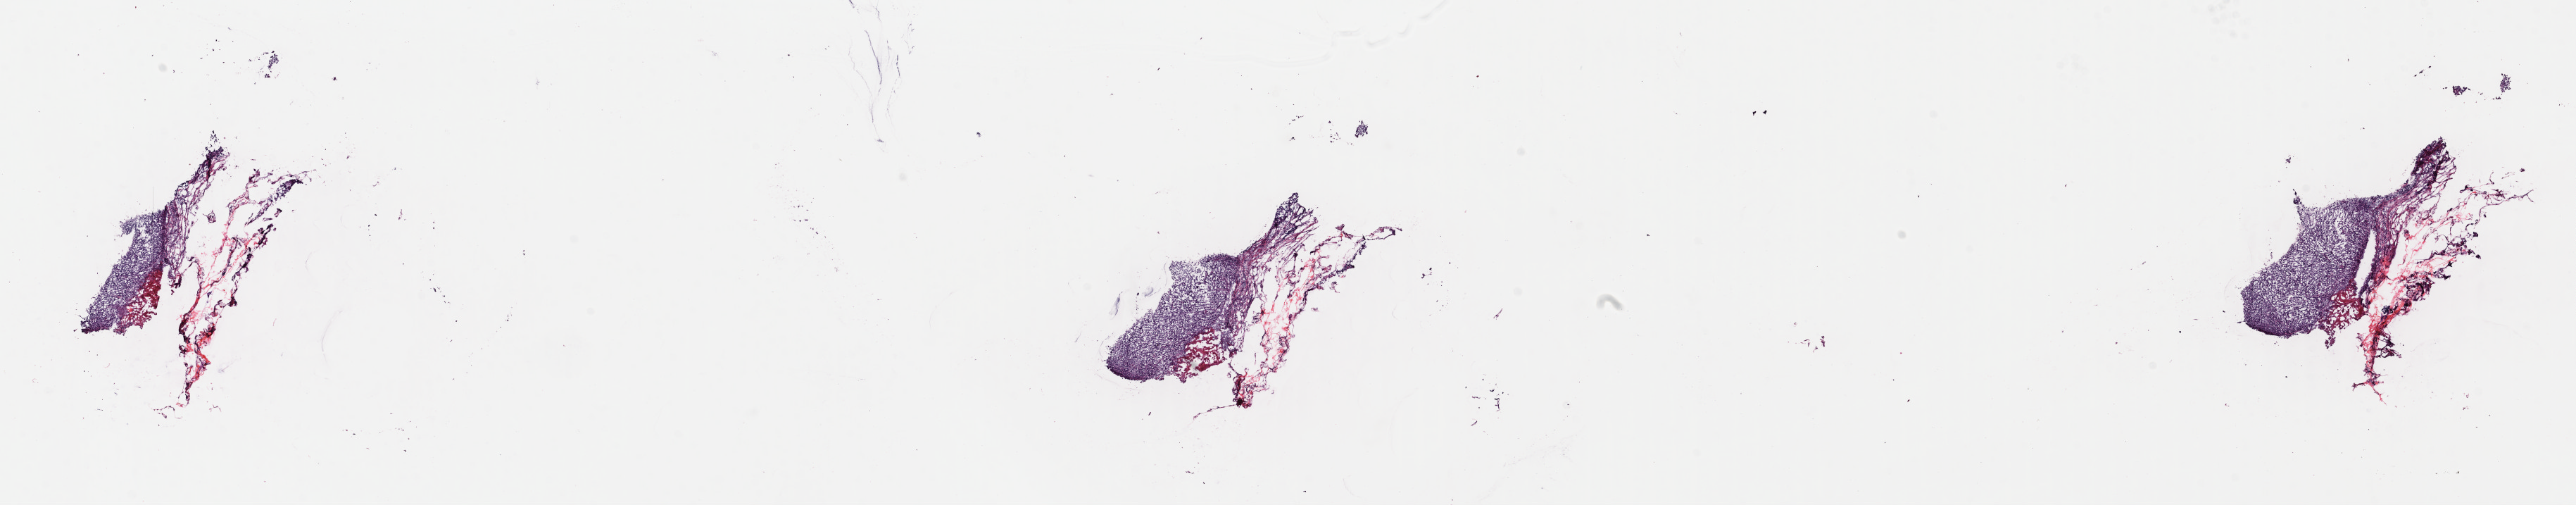
Whole-slide histology image, H&E-stained, shown as a low-resolution overview of the whole scanned area (about 28.8 x 5.6 mm, slide scanned at 40x), frozen section from the top of the tissue portion, metastatic tumour sample, sampled site not recorded. Male, age 60 years at initial diagnosis. Pathologist review of this section (percent, as recorded): tumour cells 50%, tumour nuclei 95%, normal cells 40%, stromal cells 10%, necrosis 0%. Inflammatory infiltration, as recorded: lymphocyte infiltration 0%, monocyte infiltration 0%, neutrophil infiltration 0%.
This section: metastatic tumour tissue. Patient diagnosis: Malignant melanoma, NOS.